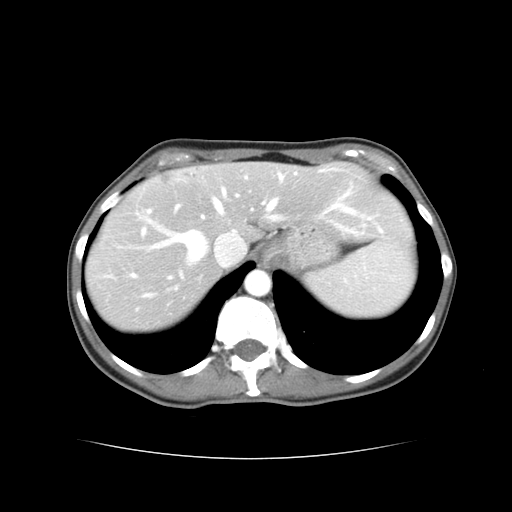
Contrast-enhanced abdominal CT, one axial slice. Slice 31 of 38 in the series (ordered by position). Reconstruction kernel STANDARD. 120 kVp. Soft-tissue window (W 400 / L 40 HU). 512 × 512 image matrix. Female patient, age 54 years. From the clinical record (not read from this slice): diagnosis: colorectal cancer liver metastases, imaged before liver resection; multiple liver metastases: yes; largest metastasis: 1.1 cm; disease in both lobes: yes.
Outlined on this slice (outlined manually by an expert reader):
- hepatic veins: bounding box (x1, y1, x2, y2) in pixels: (164, 183, 333, 261)
- liver: (88, 165, 406, 329)
- planned liver remnant (the part of the liver to remain after resection): (206, 165, 406, 238)
- portal vein (with intrahepatic branches): (142, 206, 205, 251)
- liver metastasis: (328, 184, 335, 191)